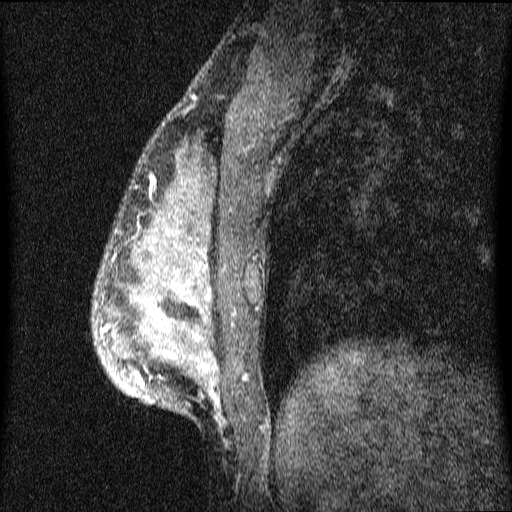
Breast MRI (dynamic contrast-enhanced), one sagittal slice; slice 19 of 64 in the series (ordered by position); dynamic contrast-enhanced series, image 2 of 4 at this slice position (ordered by acquisition); 1.5 T; TE 4.2 ms, TR 9.1 ms; 2 mm slice thickness; 512 × 512 image matrix, field of view 180 × 180 mm. Female patient, age 33 years.
Outlined on this slice (semi-automatically segmented with operator editing):
- analysis volume of interest (the breast-tissue region the enhancement analysis was run in; not a lesion): bounding box <93,151,328,426> (left, top, right, bottom; pixels)
- tumour enhancement mask (voxels above the 70 % enhancement threshold inside the analysis volume of interest): <101,178,220,407>